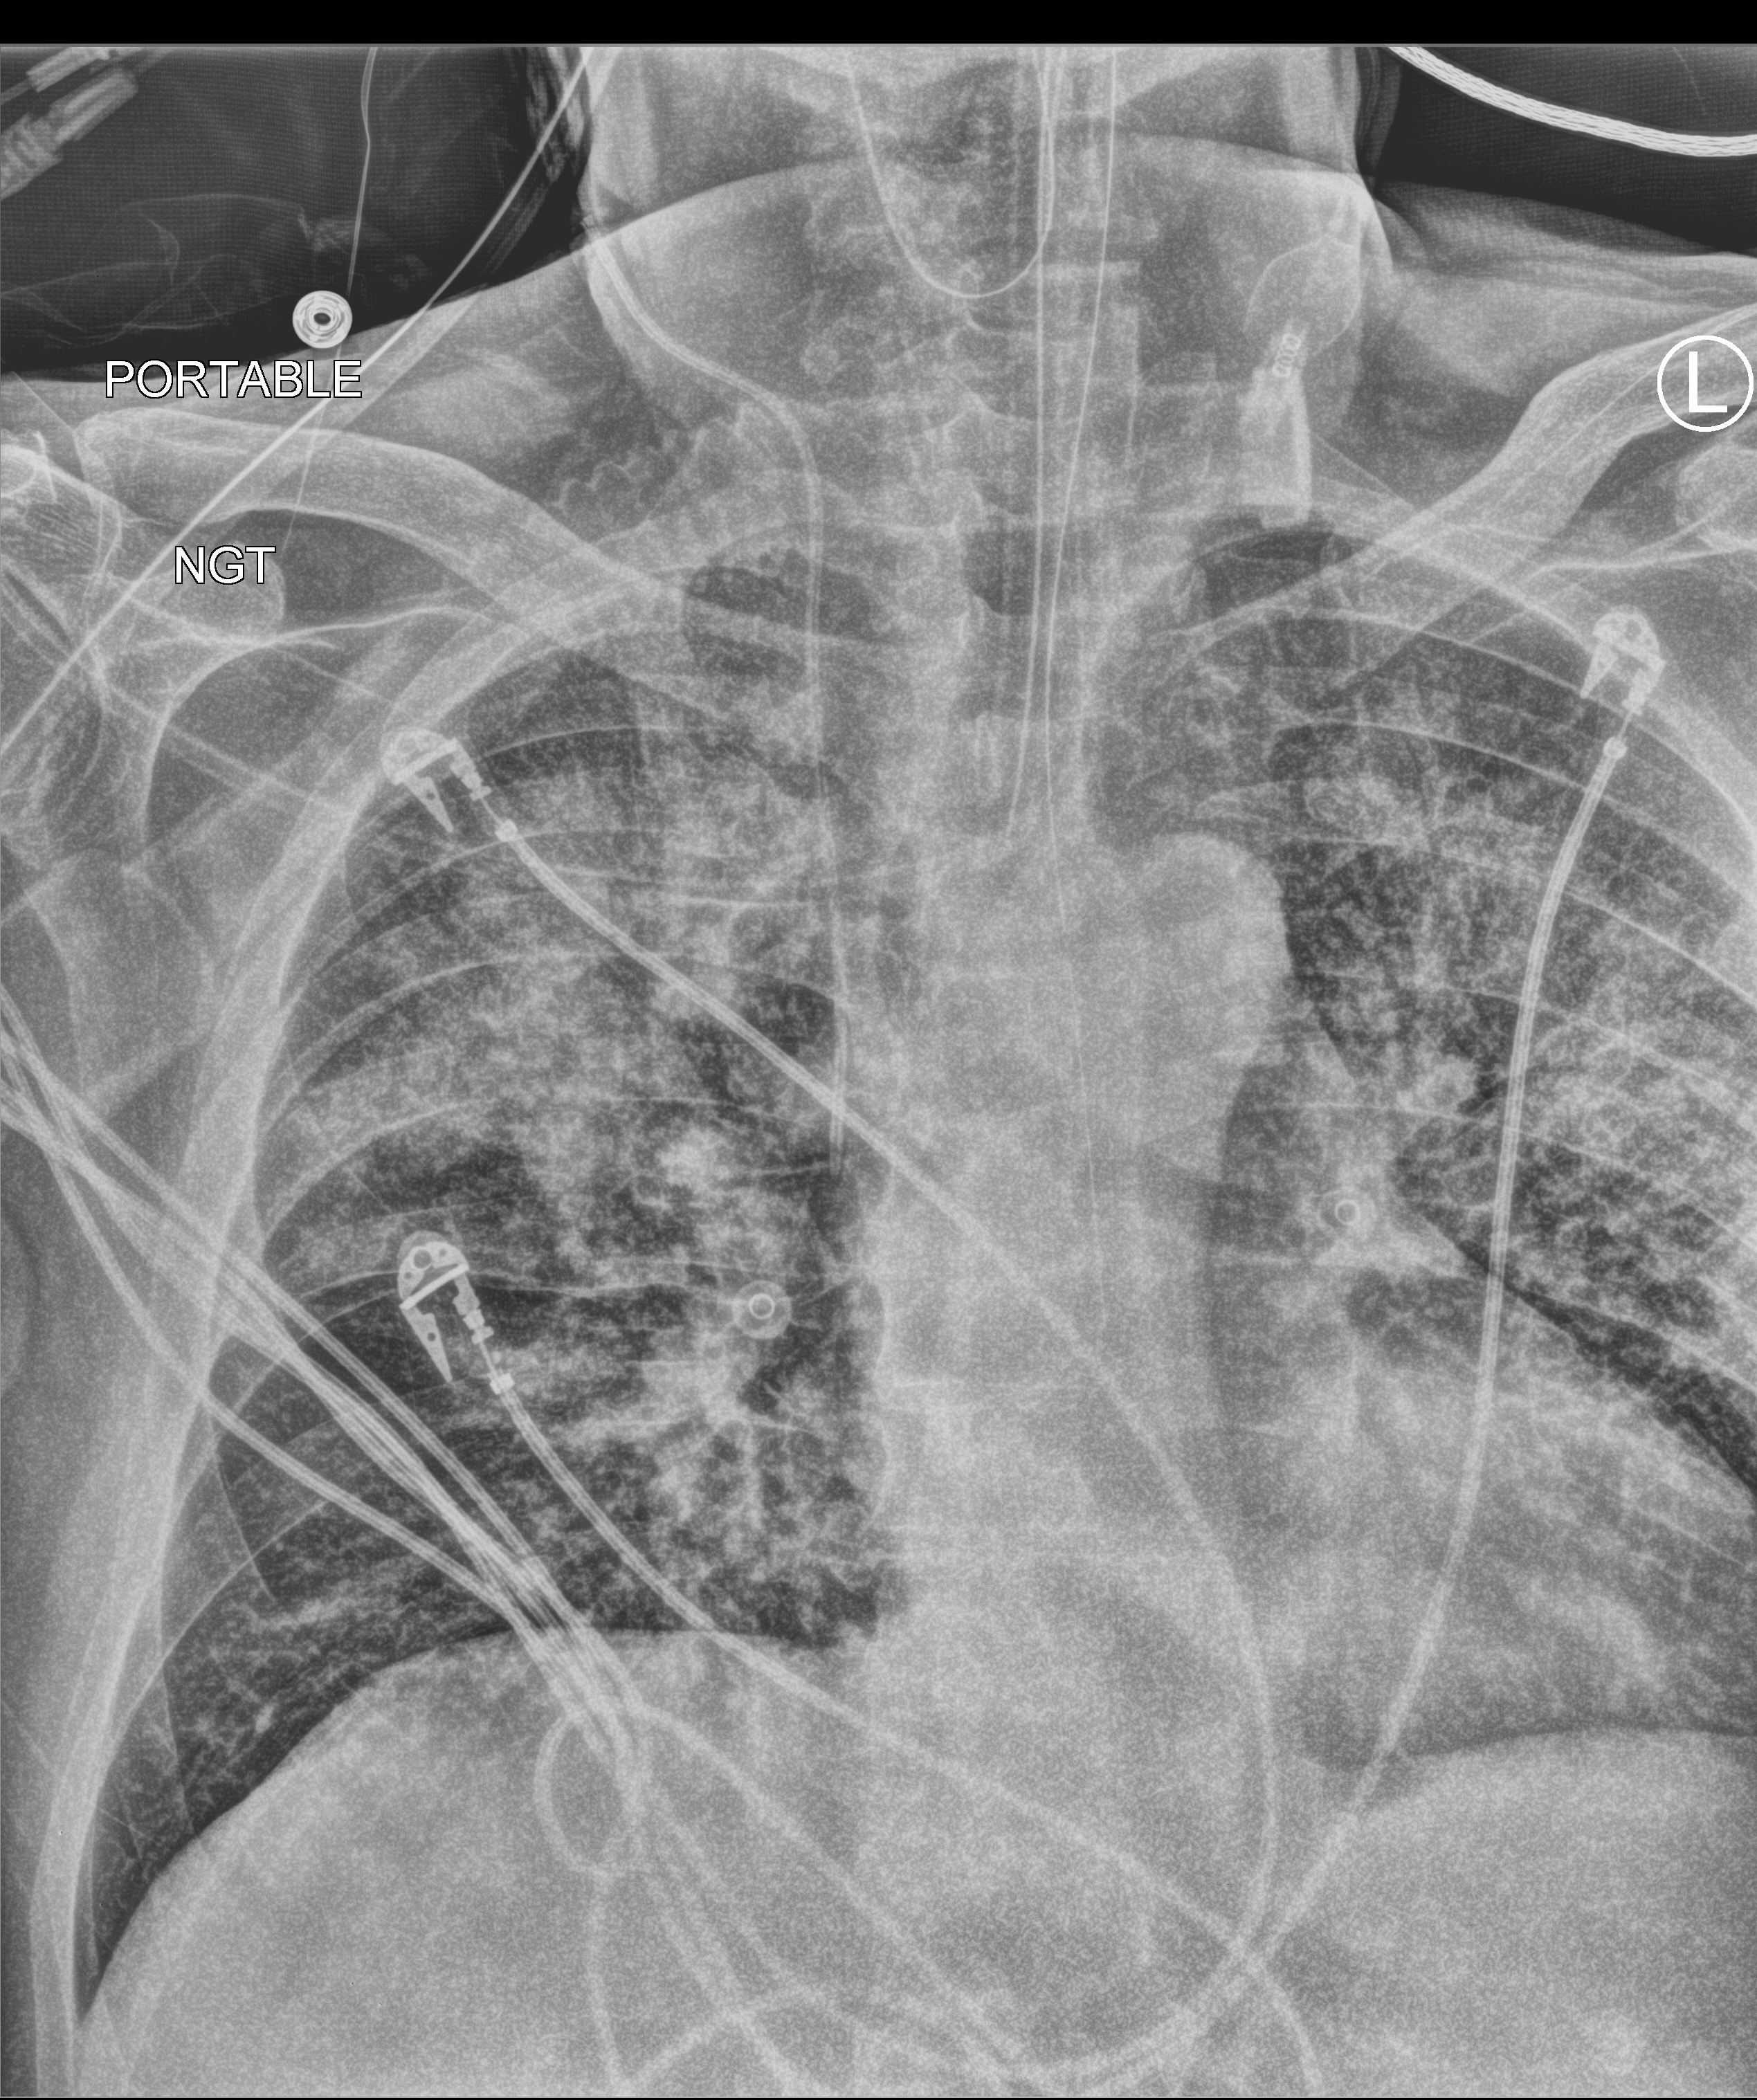
Portable chest radiograph. Male patient hospitalised with COVID-19, age 75–90 years.
From the hospital-stay record, not from the radiograph (when in the stay this image was taken is not recorded): diabetes (admission record): no.